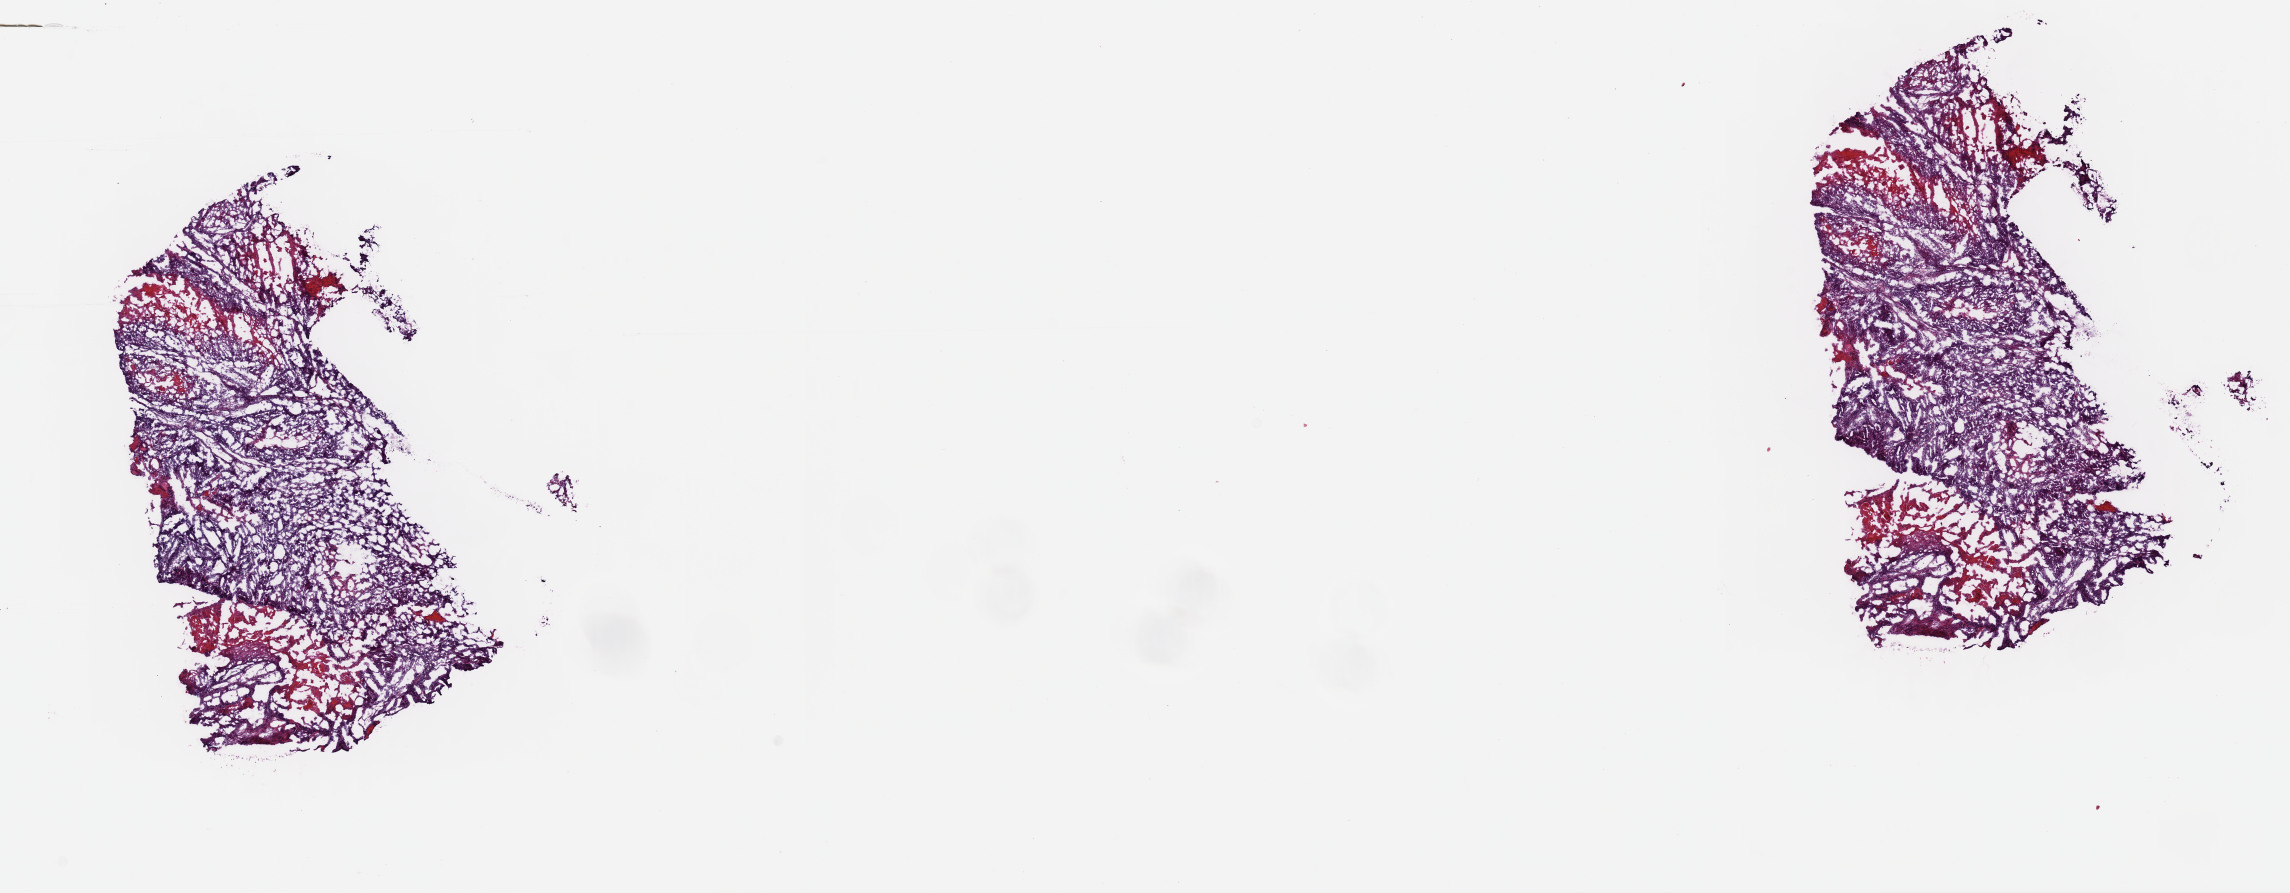
Whole-slide histology image, H&E-stained, shown as a low-resolution overview of the whole scanned area (about 18.1 x 7.1 mm, slide scanned at 40x). Frozen section from the top of the tissue portion. Uterus, primary tumour sample. Patient: female, age at initial diagnosis 72 years. Histologic grade: G3 (poorly differentiated). Pathologist review of this section (percent, as recorded): tumour cells 80%, tumour nuclei 80%, normal cells 0%, stromal cells 10%, necrosis 10%. Inflammatory infiltration, as recorded: lymphocyte infiltration 40%, monocyte infiltration 20%, neutrophil infiltration 20%.
FIGO stage: II. Histologic diagnosis: Endometrioid adenocarcinoma, NOS (endometrium).